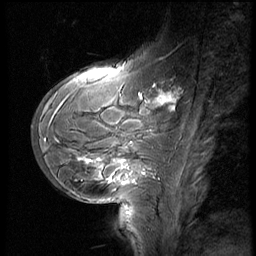
Breast MRI (dynamic contrast-enhanced), one sagittal slice. Position 19 of 60 along the scan axis. 3 images stored at this slice position (order not interpretable as contrast timing). 1.5 T. TE 4.2 ms, TR 8.9 ms. 2.5 mm slice thickness. 256 × 256 image matrix, field of view 200 × 200 mm. Female patient, age 29 years. From the clinical record (not read from this slice): setting: breast cancer imaged before/during neoadjuvant chemotherapy.
Annotated regions visible in this slice (semi-automatically segmented with operator editing):
- analysis volume of interest (the breast-tissue region the enhancement analysis was run in; not a lesion): bounding box [x1, y1, x2, y2] px = [33, 57, 185, 200]
- tumour enhancement mask (voxels above the 140 % enhancement threshold inside the analysis volume of interest): [80, 86, 173, 184]